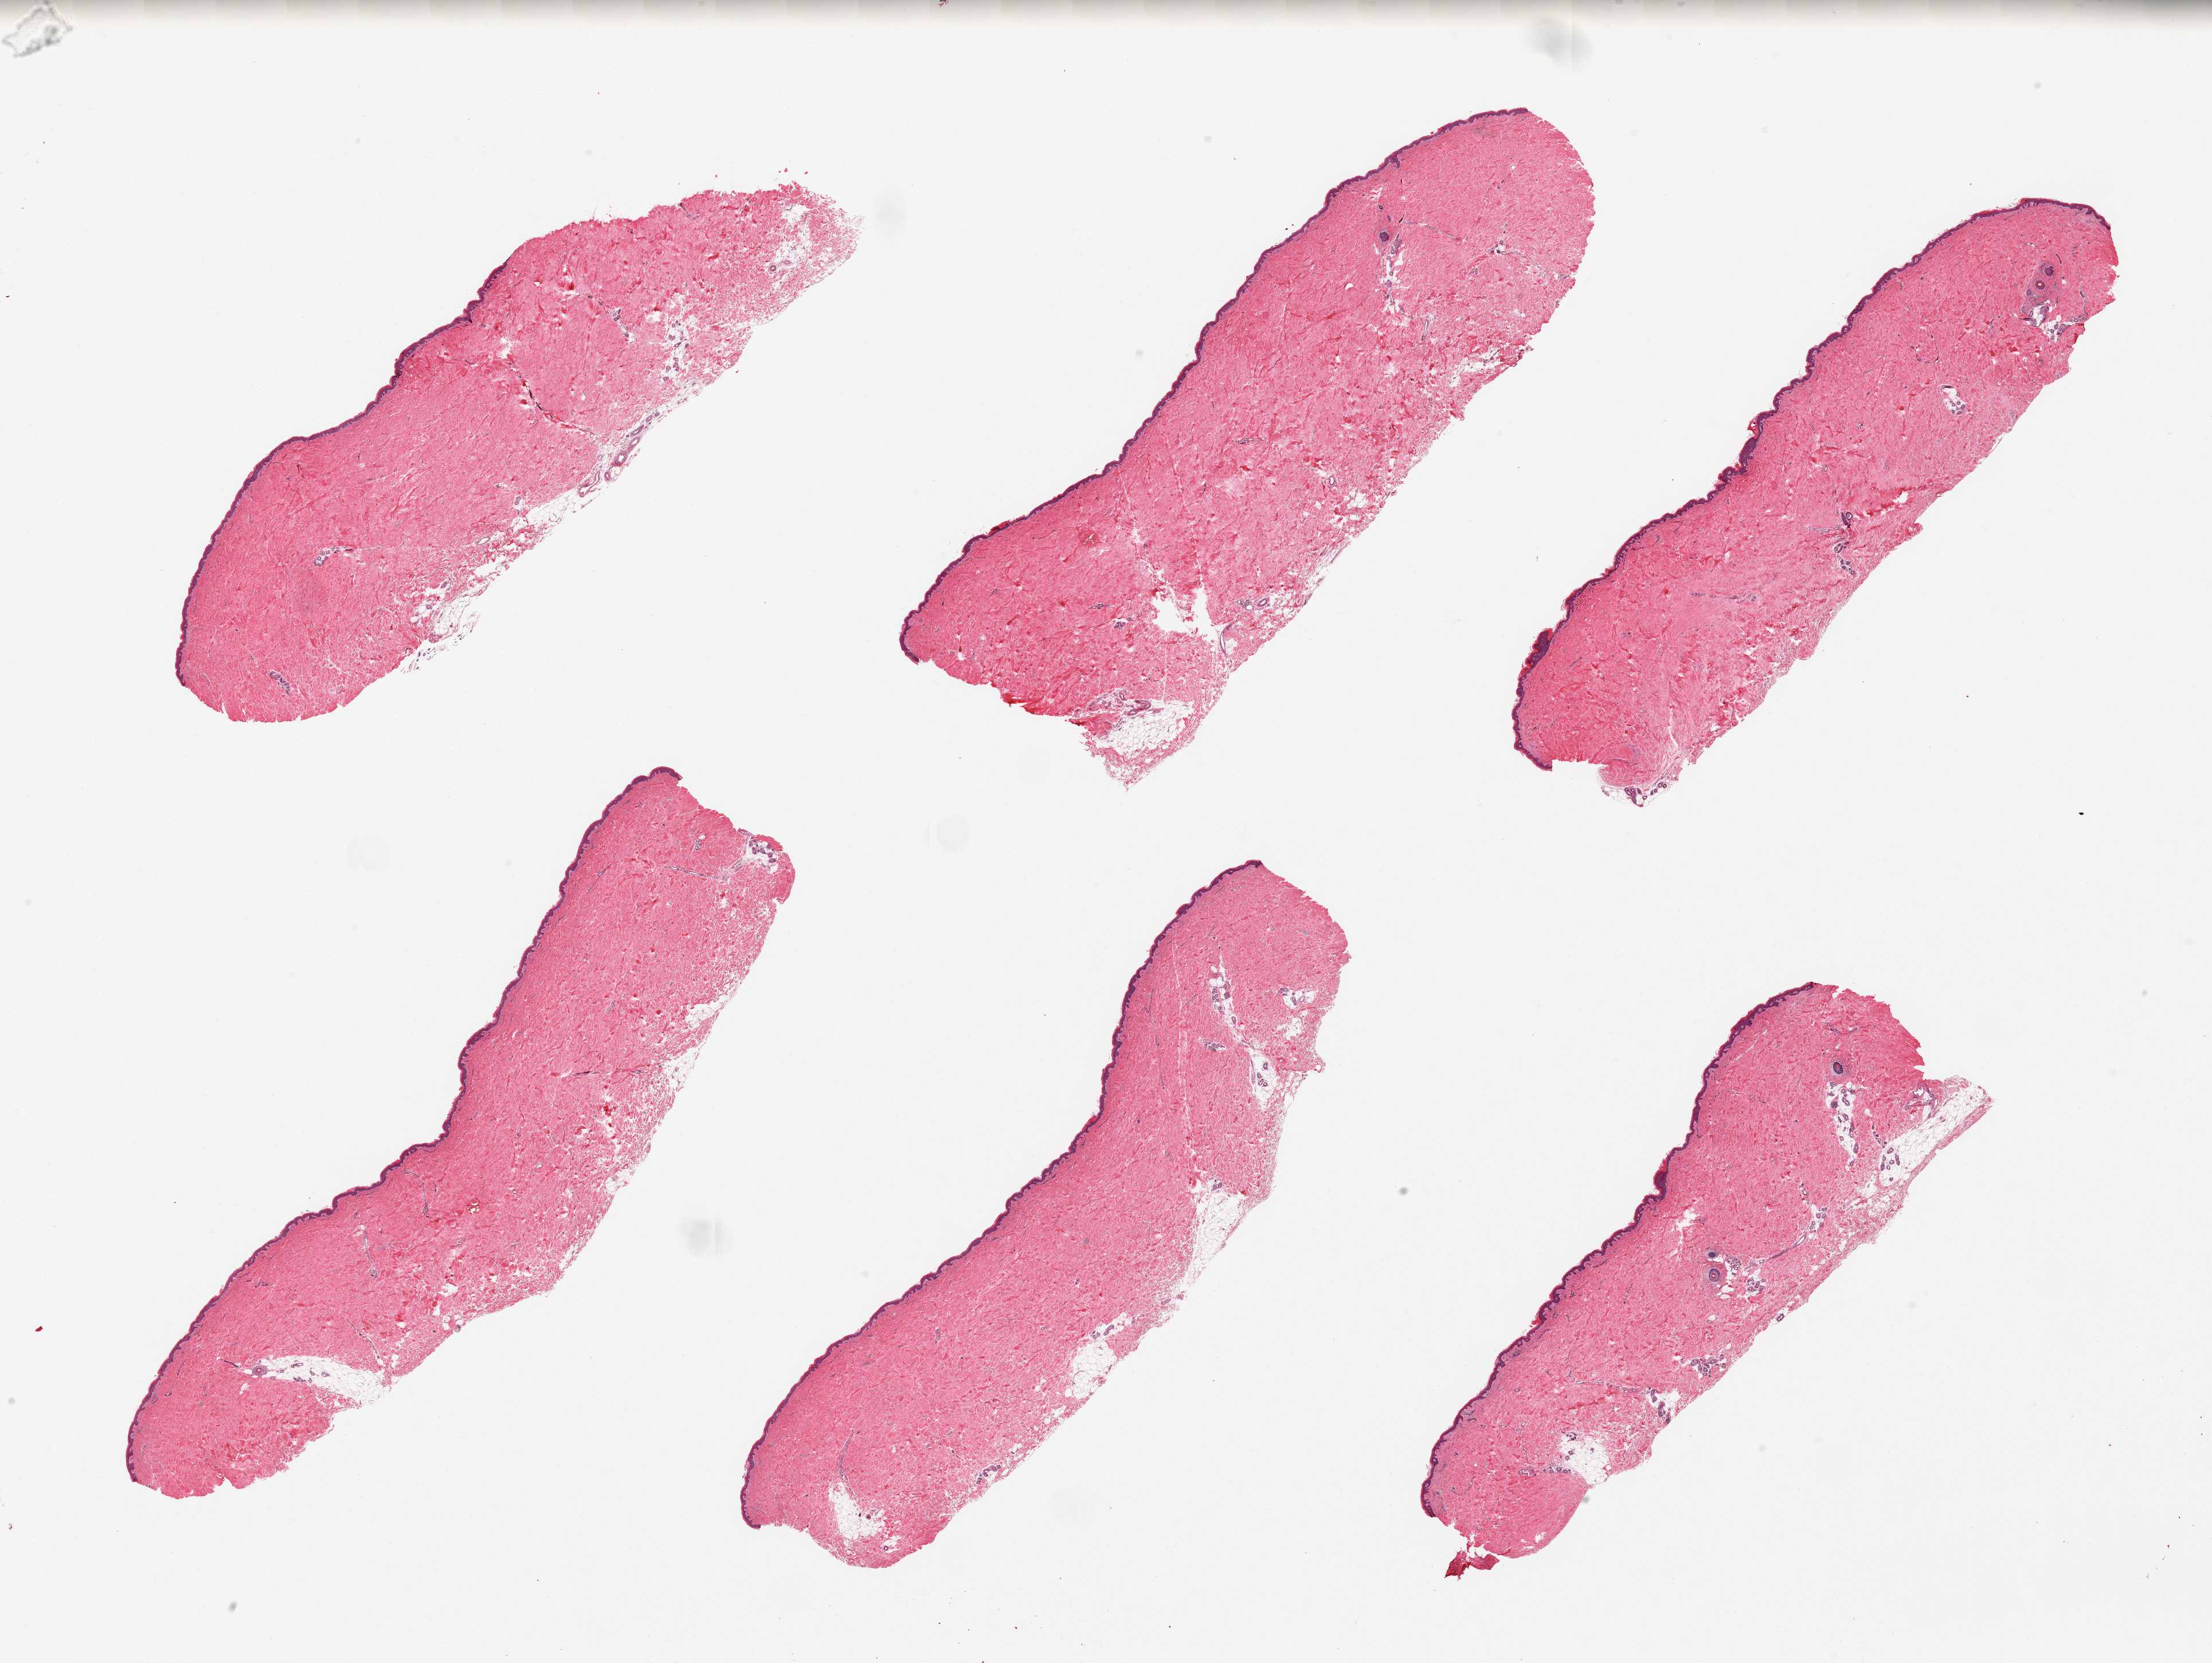
Haematoxylin and eosin whole-slide image — whole scanned area (about 30.5 x 22.9 mm, acquisition: 20x scan) shown as a low-resolution overview, PAXgene-fixed paraffin-embedded (PFPE) section, section of skin of suprapubic region (target tissue), donor tissue sample.
Reviewer comment on this tissue sample: 6 pieces, minimal dermal fat, sqaumous epithelium is ~60 microns.